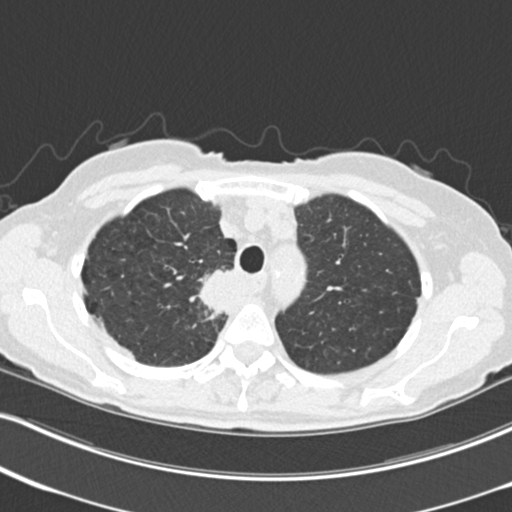
Low-dose screening chest CT, one axial slice; position 176 of 226 along the scan axis; reconstruction kernel B30f; 120 kVp; lung window (W 1500 / L -600 HU); 2 mm slice thickness; 512 × 512 image matrix, field of view 322 × 322 mm.
Structures marked on this image (outlined manually by an expert reader):
- lesion 1 (tumor, mediastinum): bounding box <199,269,235,316> (left, top, right, bottom; pixels)